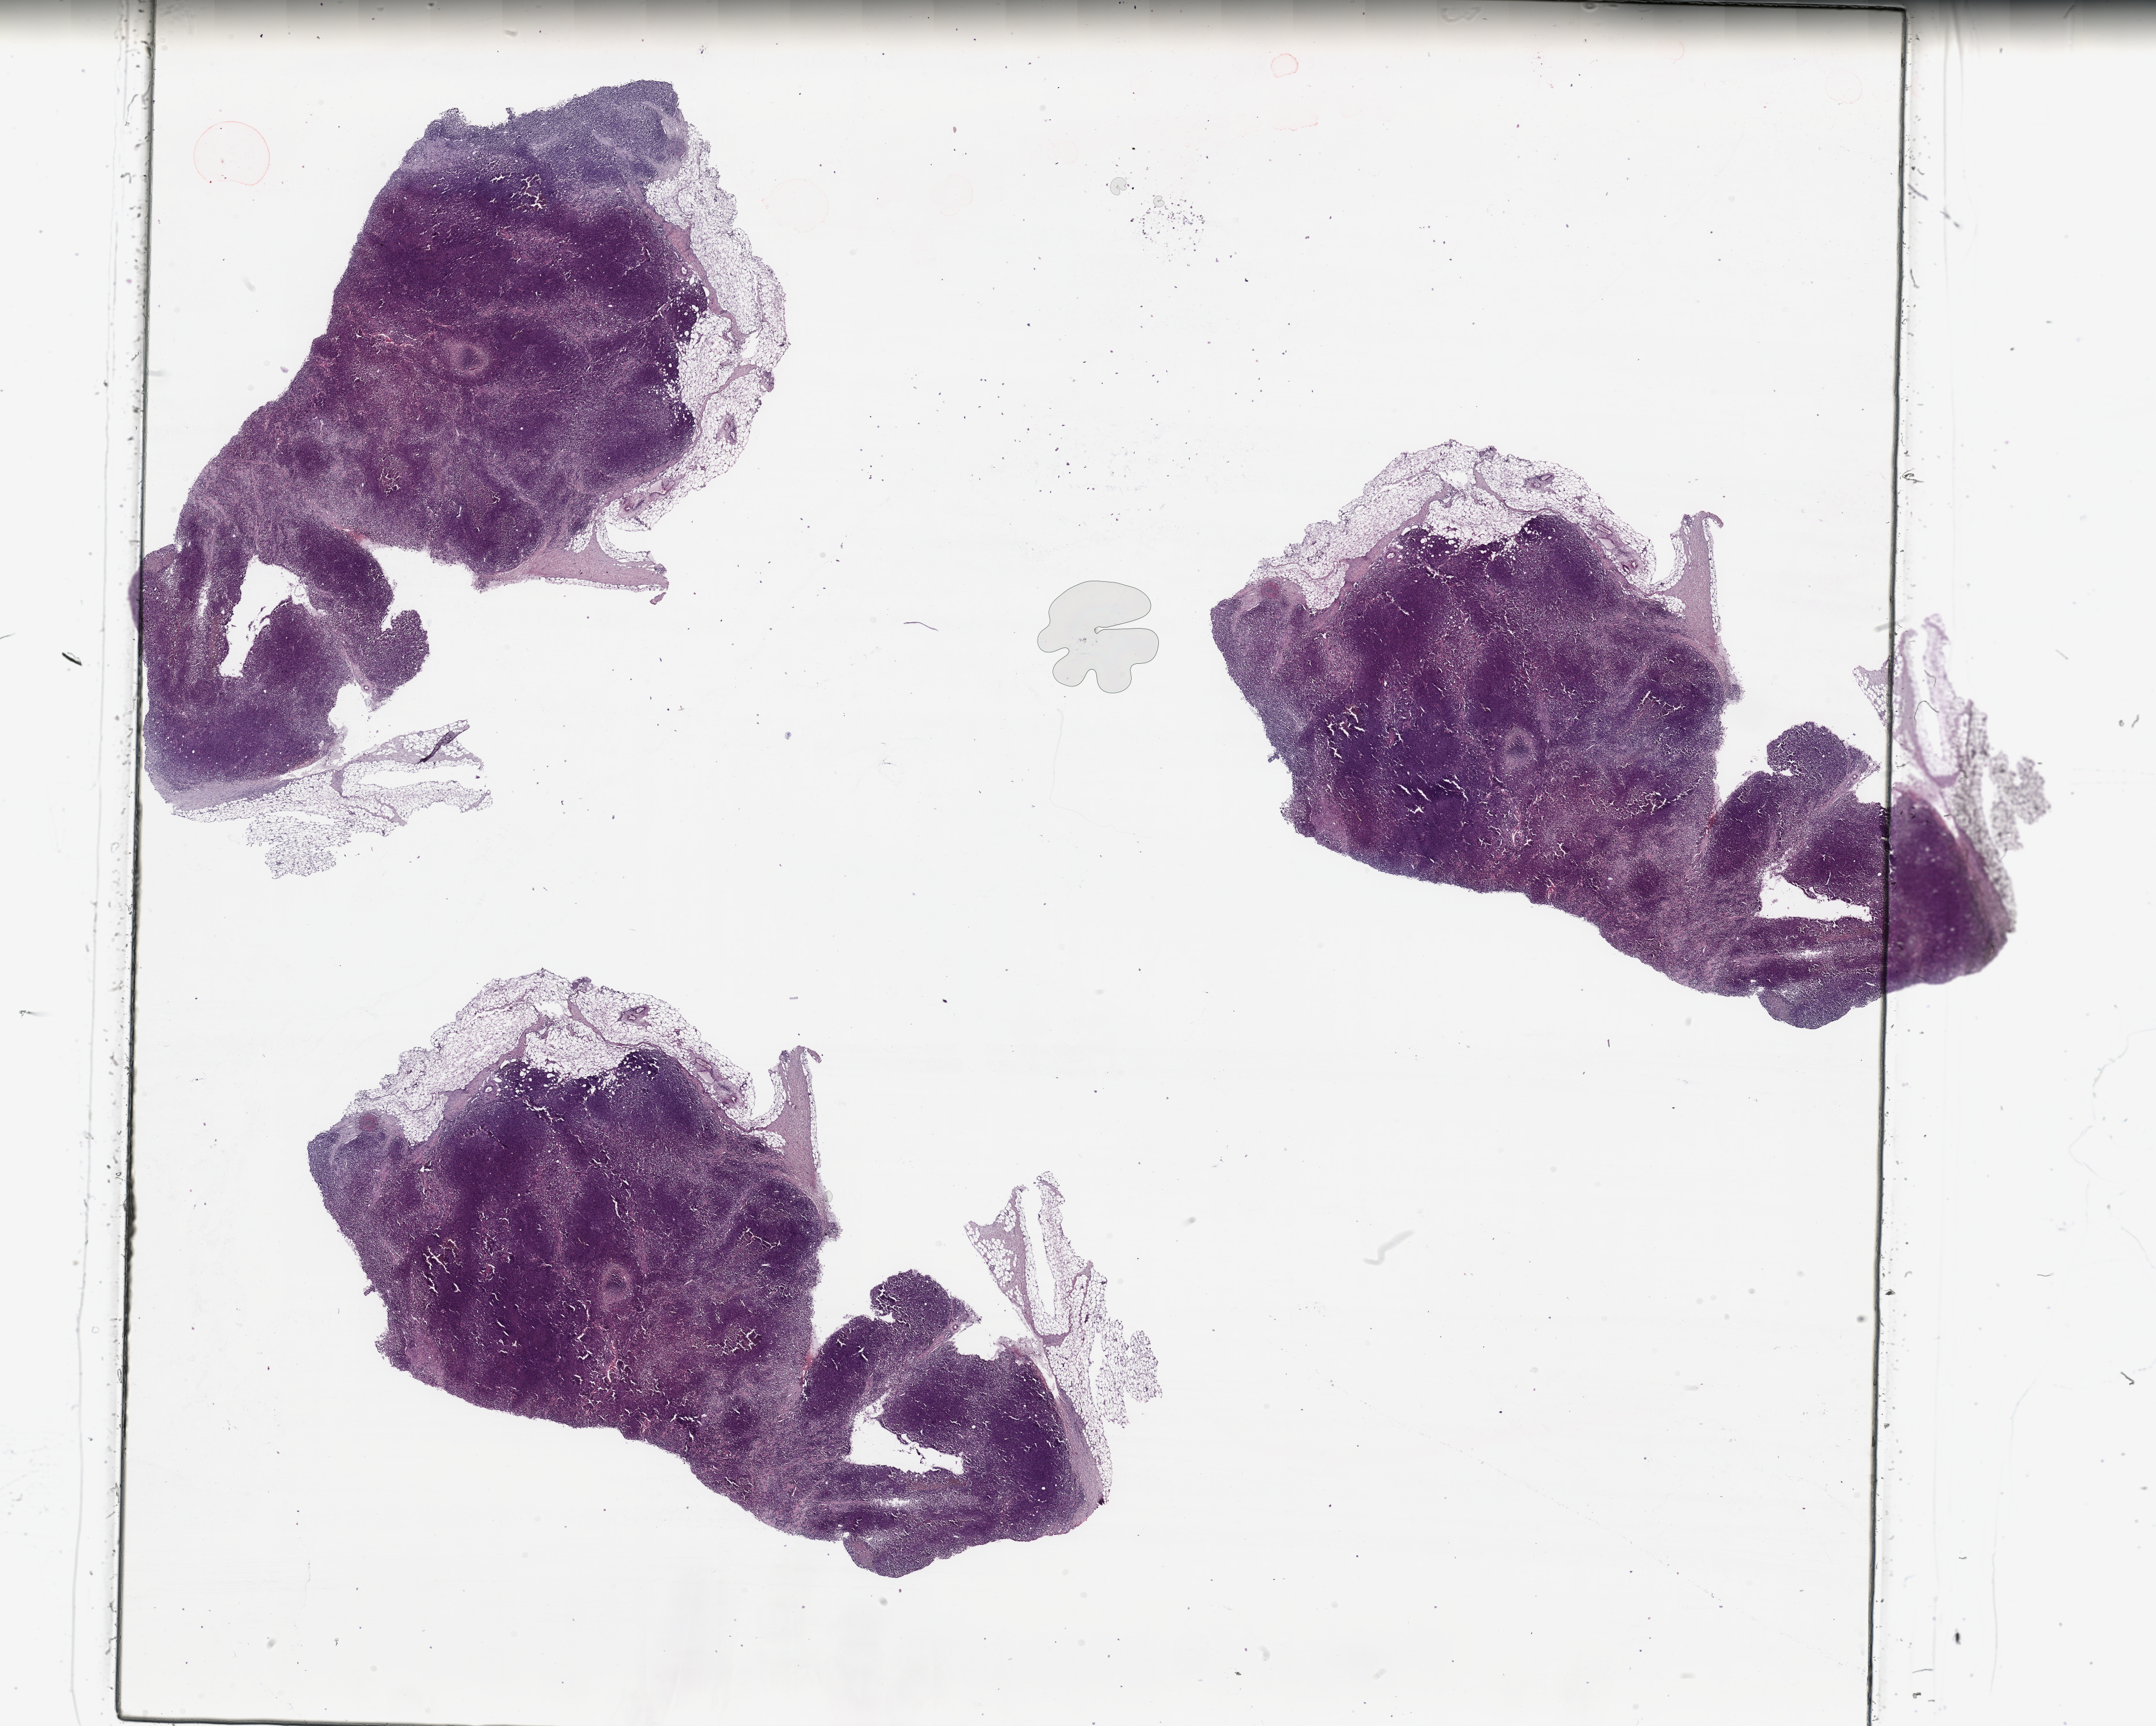
Digitized Hematoxylin and eosin (H&E) stained tissue section (whole slide) — a low-resolution overview of the entire scanned area, about 29.5 x 23.6 mm, melanoma tumour tissue; sampled site not recorded. 45-year-old male patient.
- primary tumour site (as recorded): trunk
- diagnosis: Malignant melanoma, NOS
- AJCC pathologic stage: IIB